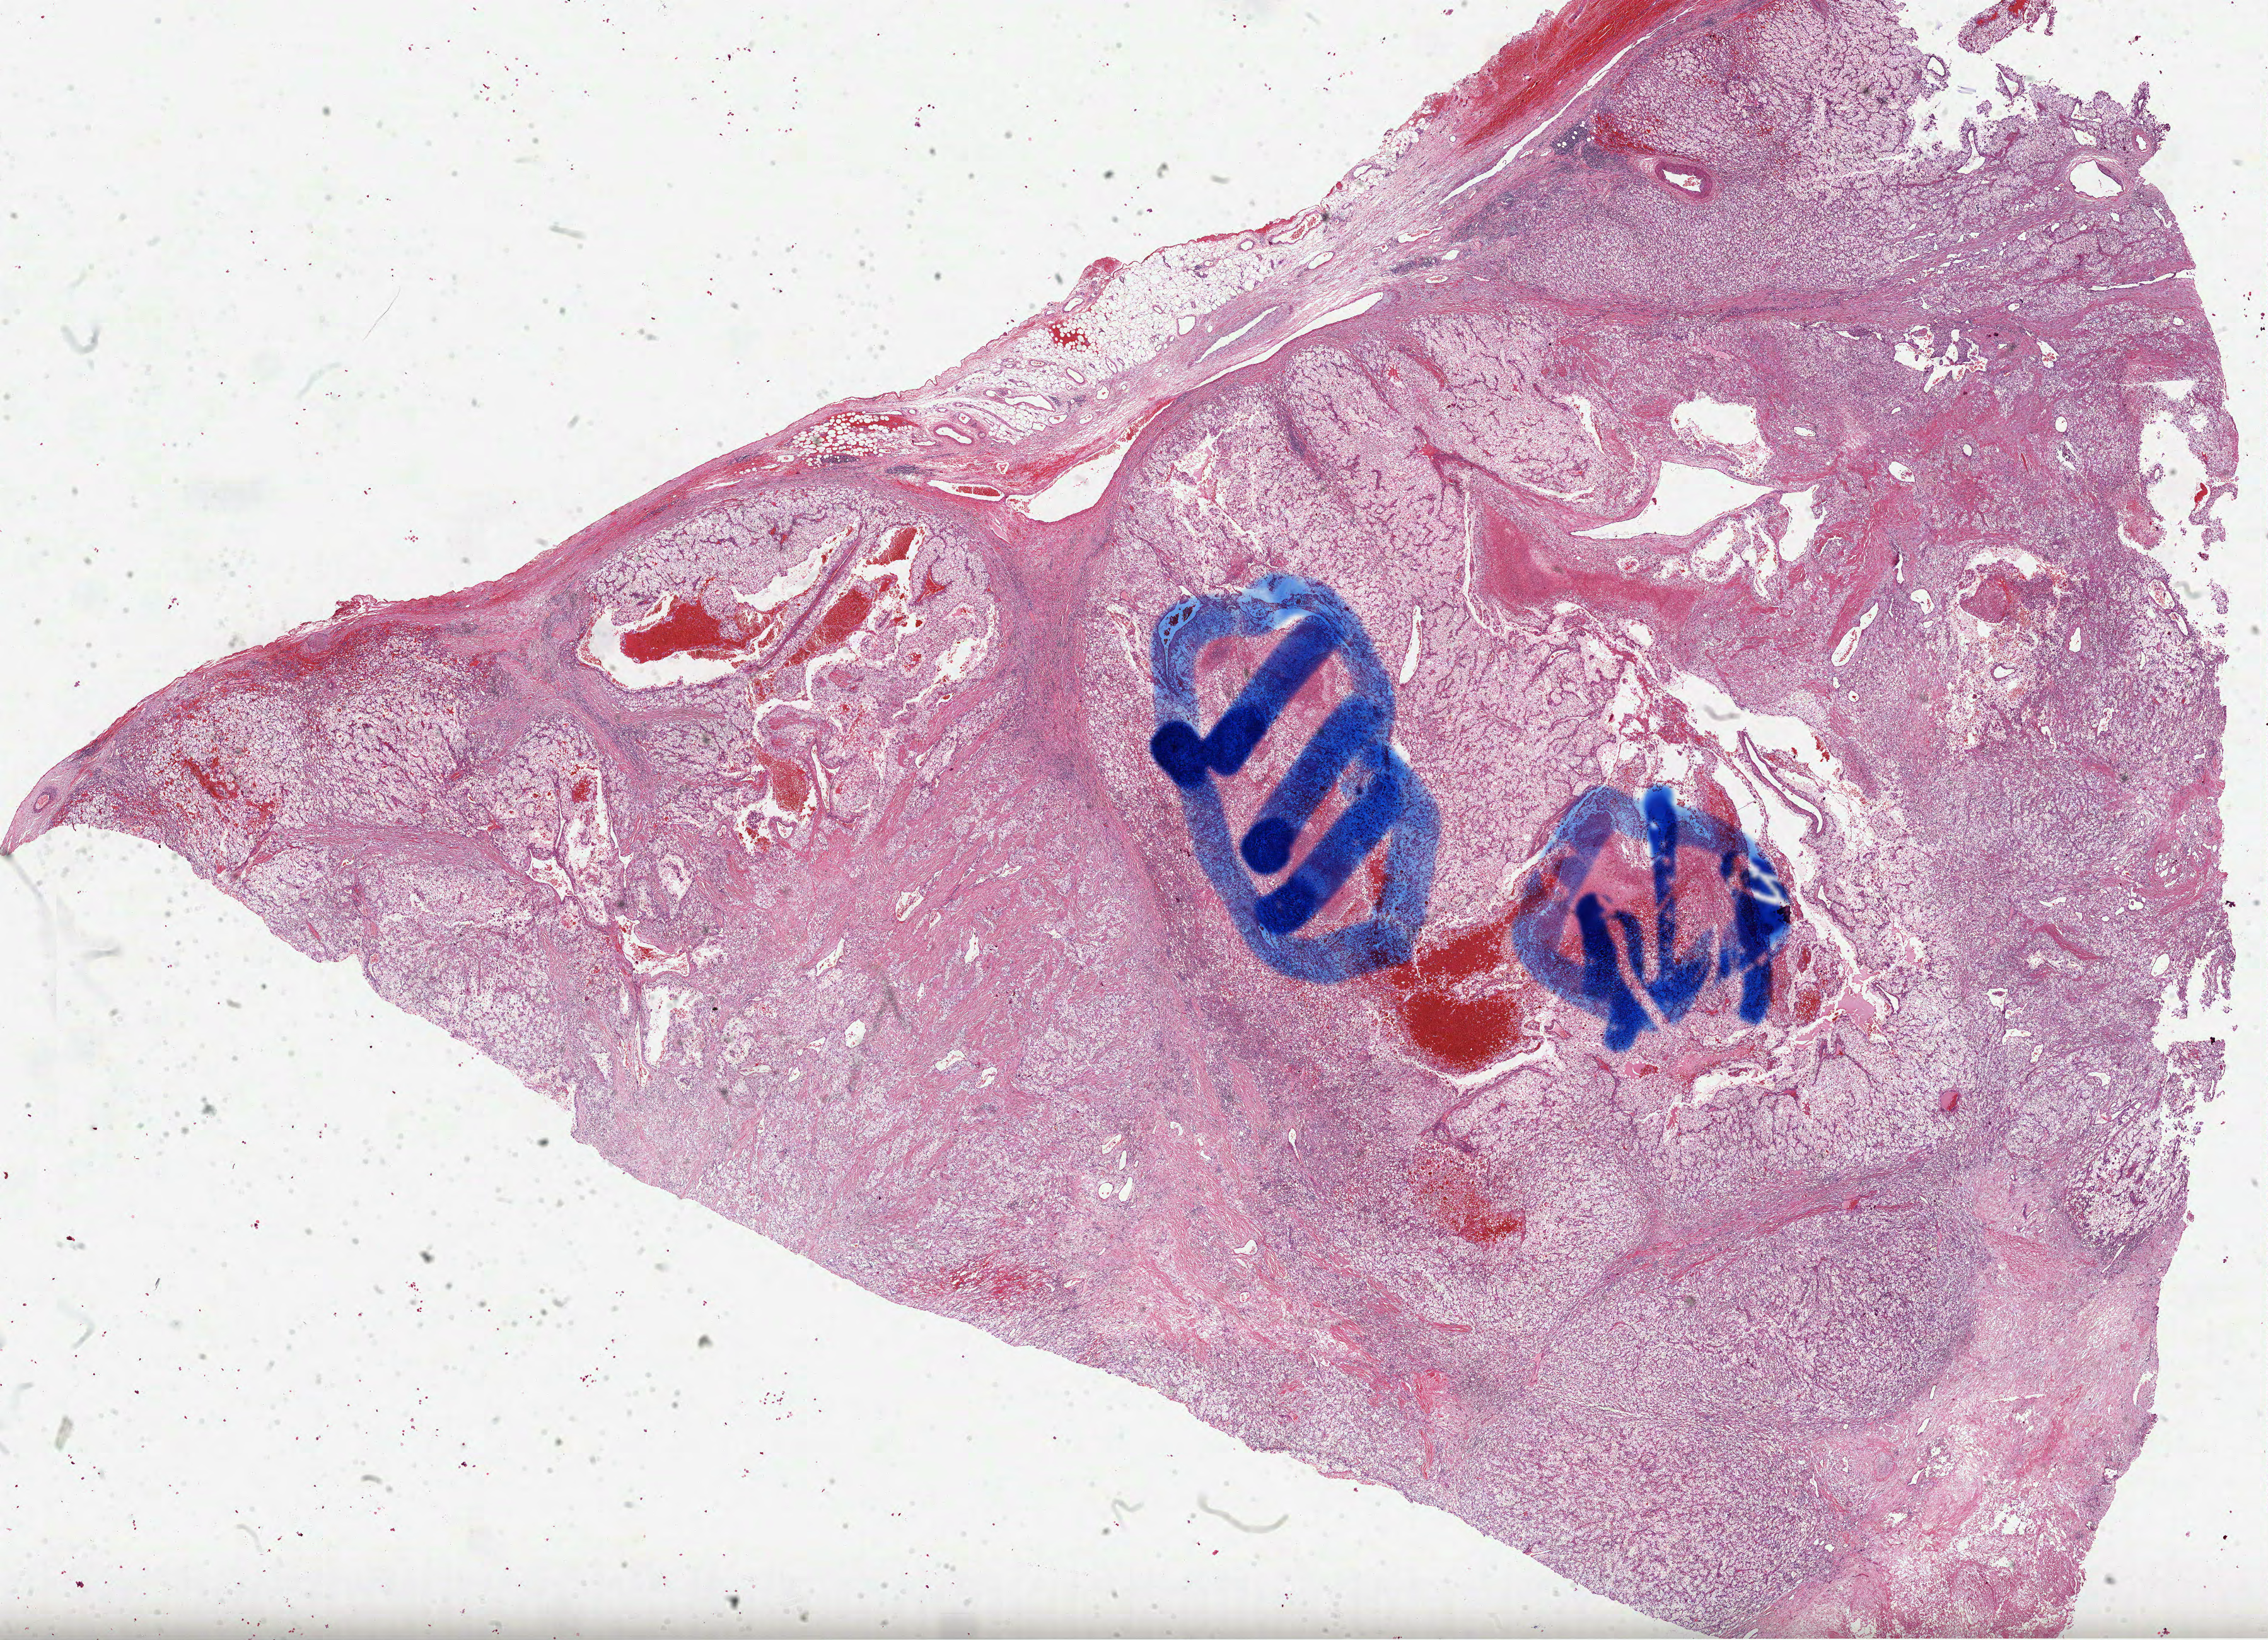
H&E-stained whole-slide image — shown as a low-resolution overview of the whole scanned area (about 29.0 x 21.0 mm); formalin-fixed paraffin-embedded (FFPE) diagnostic section; primary tumour sample from the kidney. Male, age 60 years at initial diagnosis. Histologic grade: G4 (undifferentiated).
* TNM: T4 NX M1
* diagnosis: Clear cell adenocarcinoma, NOS
* AJCC pathologic stage: IV (6th edition)